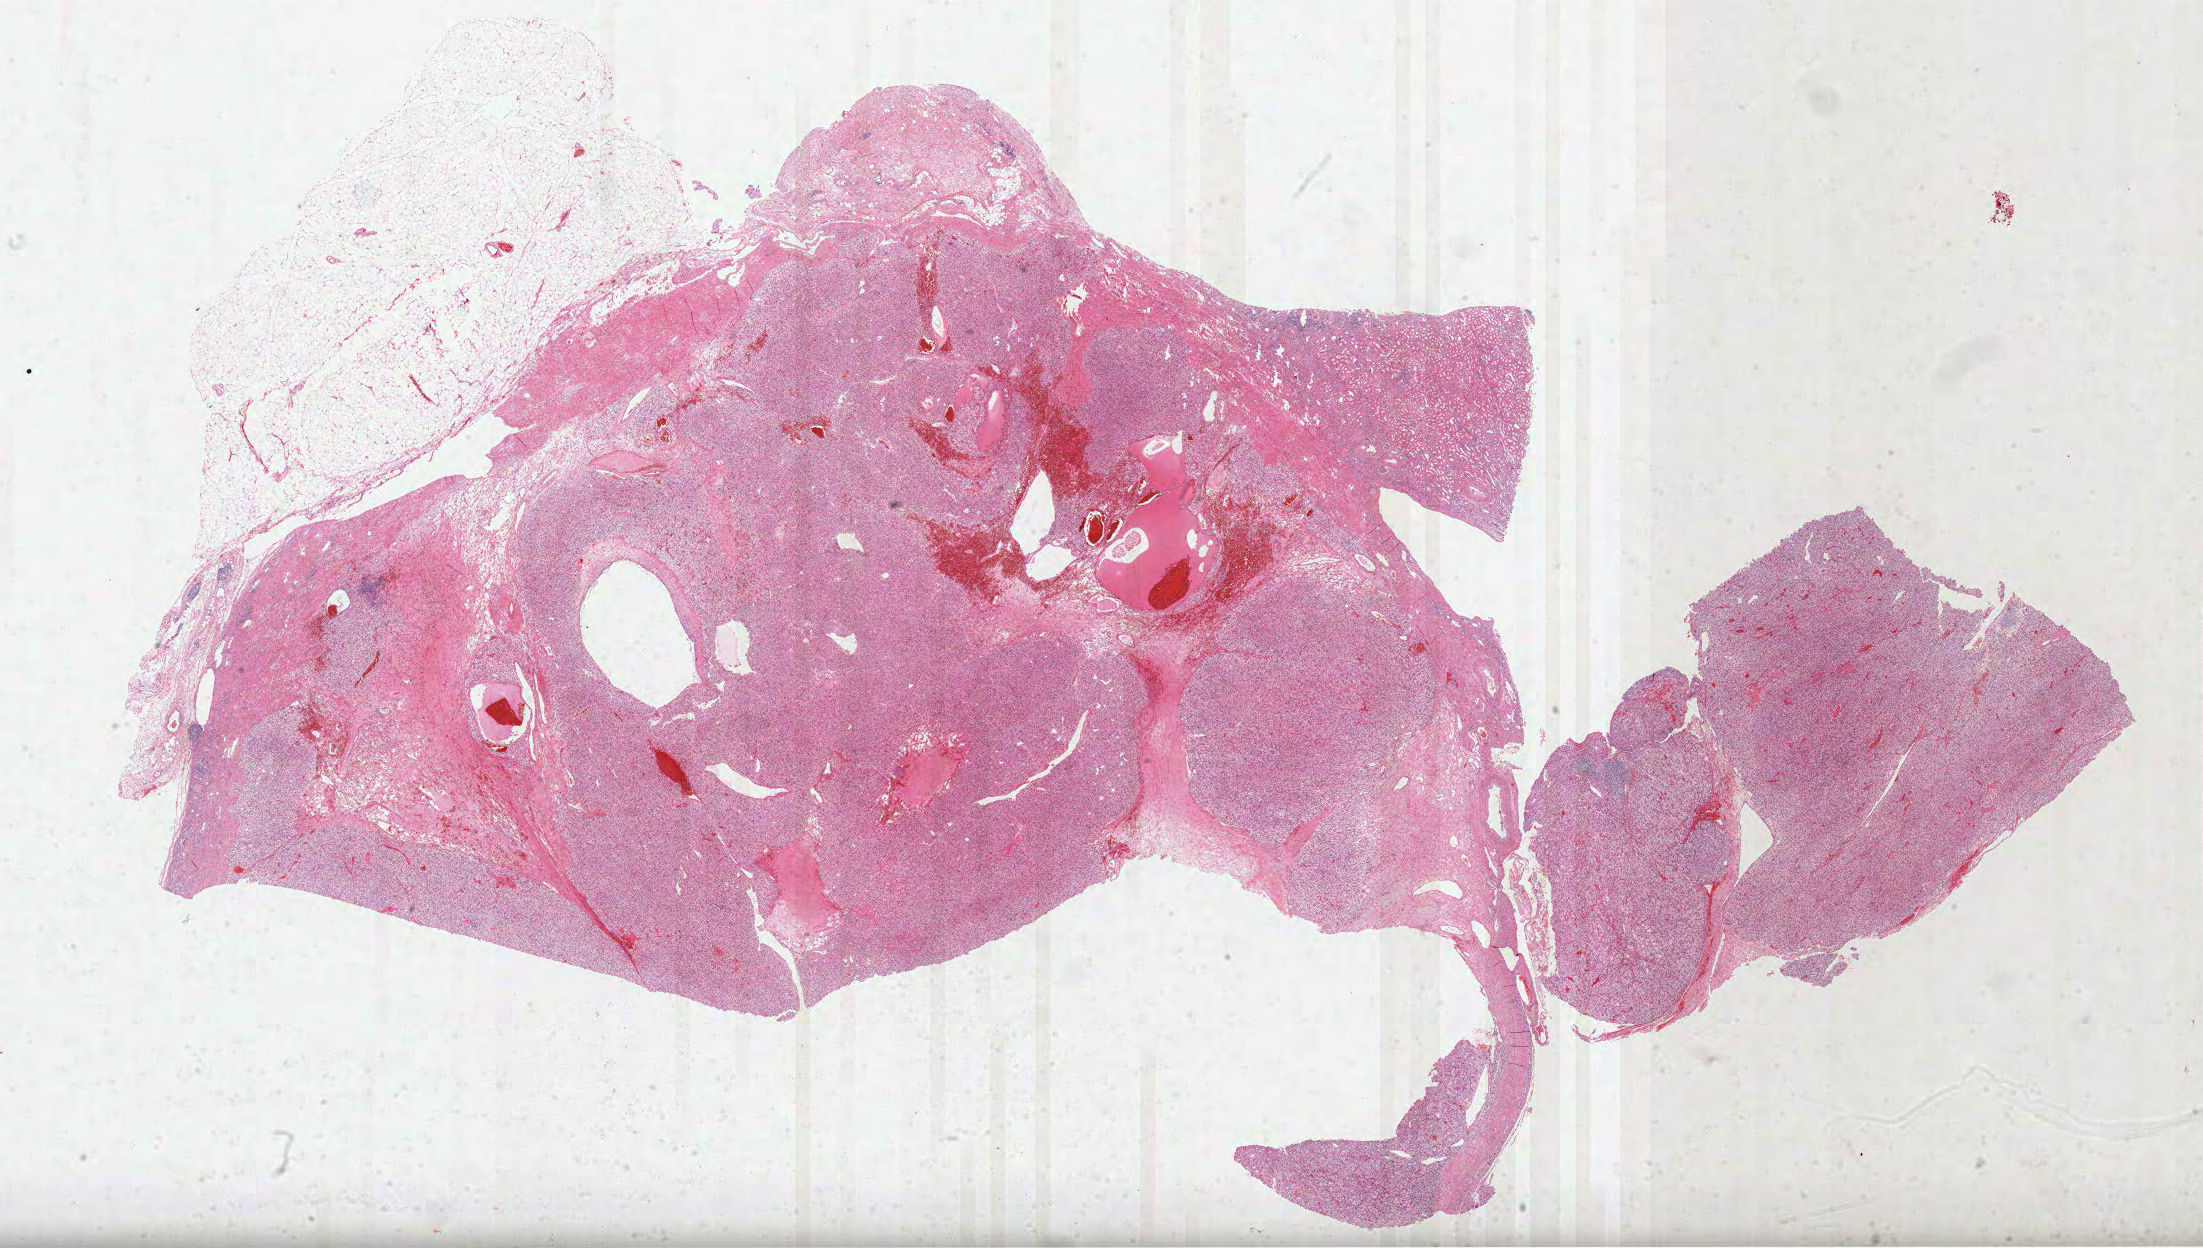
H&E-stained whole-slide image, whole scanned area (about 35.5 x 20.1 mm, slide scanned at 40x) shown as a low-resolution overview; formalin-fixed paraffin-embedded (FFPE) diagnostic section; primary tumour sample from the kidney. Female, age 82 years at initial diagnosis. Histologic grade: G2 (moderately differentiated).
Diagnosis: Clear cell adenocarcinoma, NOS. AJCC pathologic stage: I. TNM: T1b N0 M0.